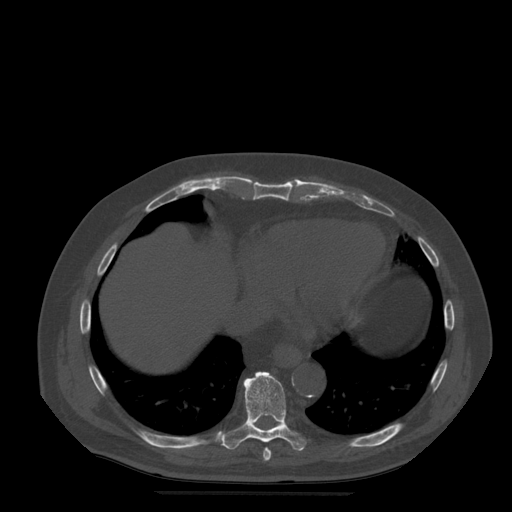
CT including the spine, one axial slice; position 292 of 522 along the scan axis; bone window (W 1800 / L 400 HU); 1.25 mm slice thickness; 512 × 512 image matrix, field of view 420 × 420 mm. Patient age 72 years. Case-level facts recorded for this patient, not image findings: primary cancer: prostate.
Annotated regions visible in this slice (semi-automatic segmentation, software-assisted and operator-edited):
- T8 vertebra: bounding box <264,448,272,461> (left, top, right, bottom; pixels)
- T9 vertebra: <222,372,308,451>